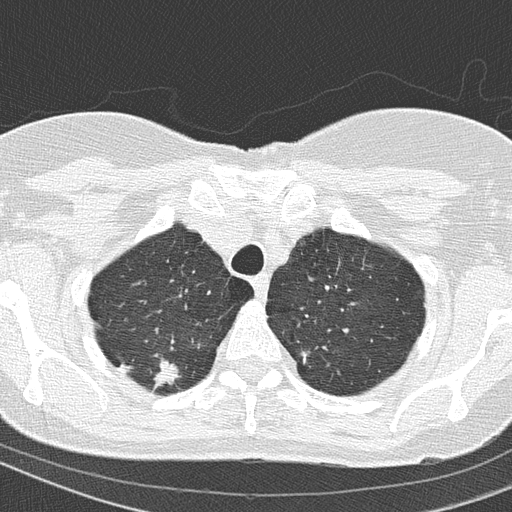
Low-dose screening chest CT, axial slice; baseline screening round; lung window (W 1500 / L -600 HU); slice 24 of 154 in the series. Female participant, aged 67 years at enrolment.
Lesion marked by an expert reader, bounding box <132,346,193,396> (left, top, right, bottom; pixels). Reader record for this screening exam (exam-level; its link to the box is not recorded): non-calcified nodule or mass ≥4 mm, right upper lobe, 15 × 14 mm, spiculated (stellate) margins, soft tissue attenuation.